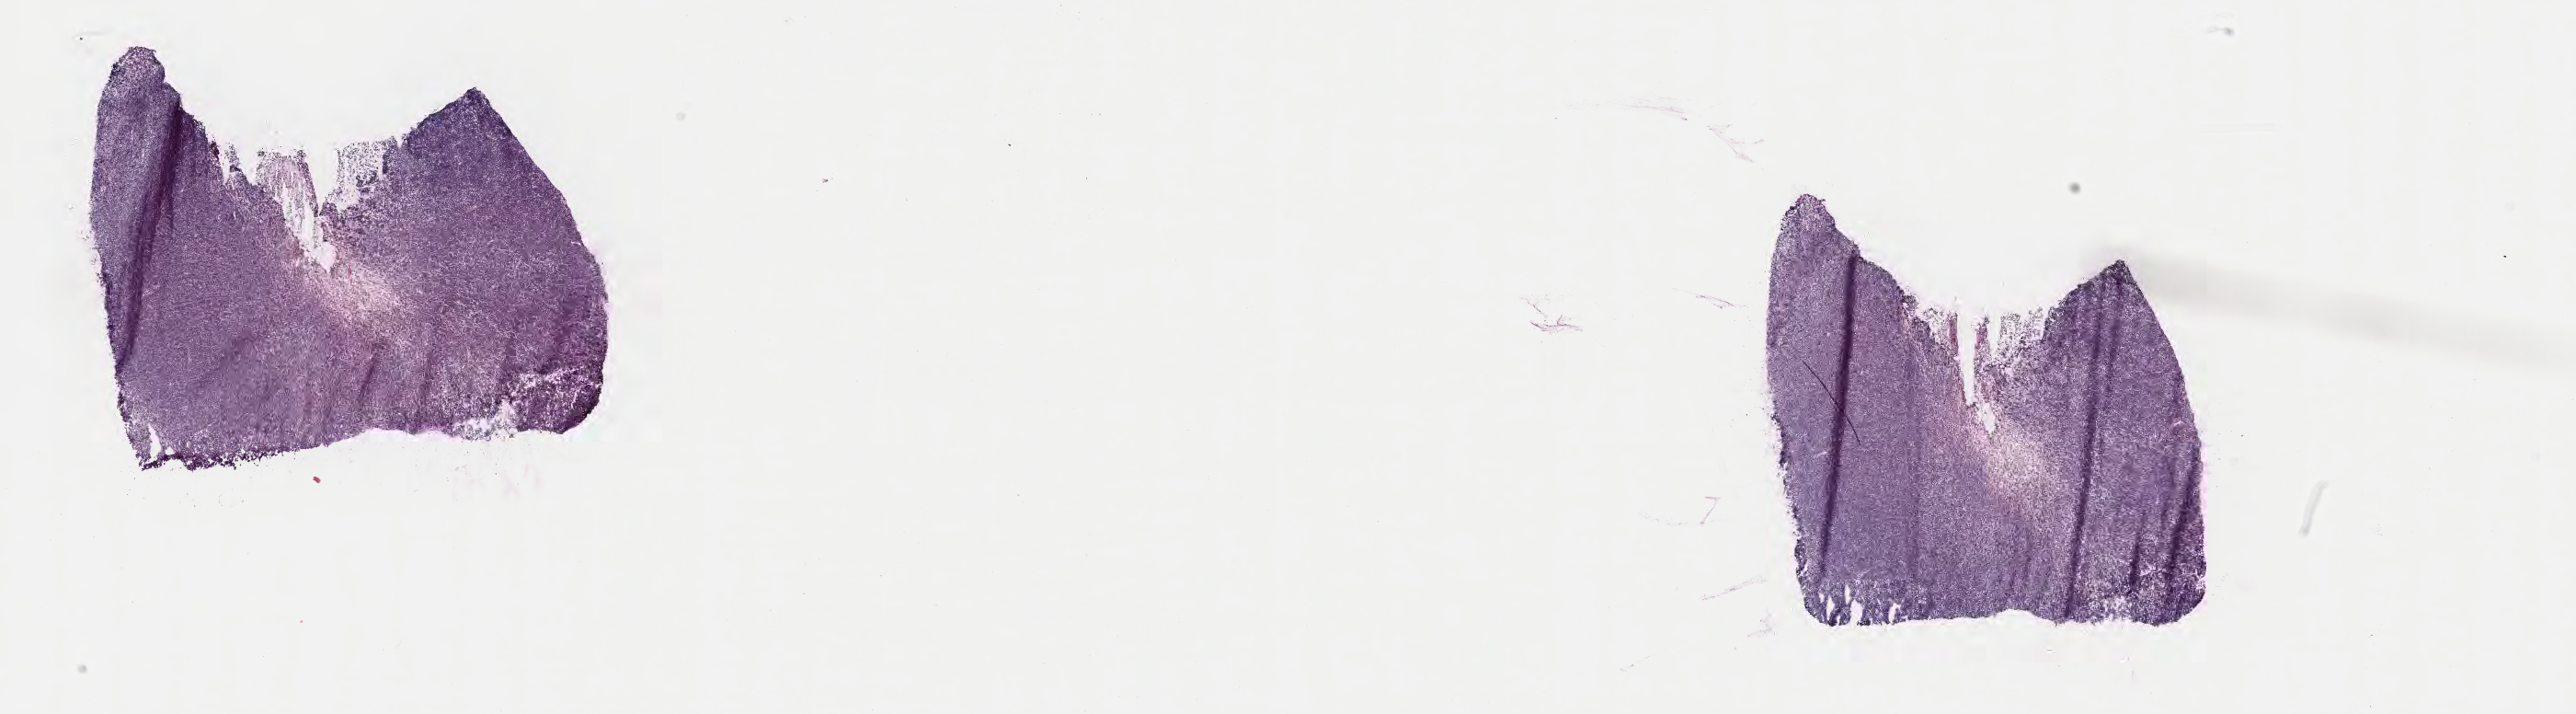
Digitized H&E-stained section, whole scanned area (about 22.7 x 6.3 mm) shown as a low-resolution overview, frozen section (tissue freezing medium), specimen: primary tumor, site: cranium. Patient male; 46 years old. Composition of this section per pathologist review: tumor cells 85%, tumor nuclei 95%, stromal cells 5%, necrosis 10%, normal cells 0%. Infiltration values recorded for this section: lymphocyte infiltration 40%, monocyte infiltration 35%, neutrophil infiltration 5%.
• Ann Arbor stage (patient): Stage IV
• histologic diagnosis: Burkitt lymphoma, NOS